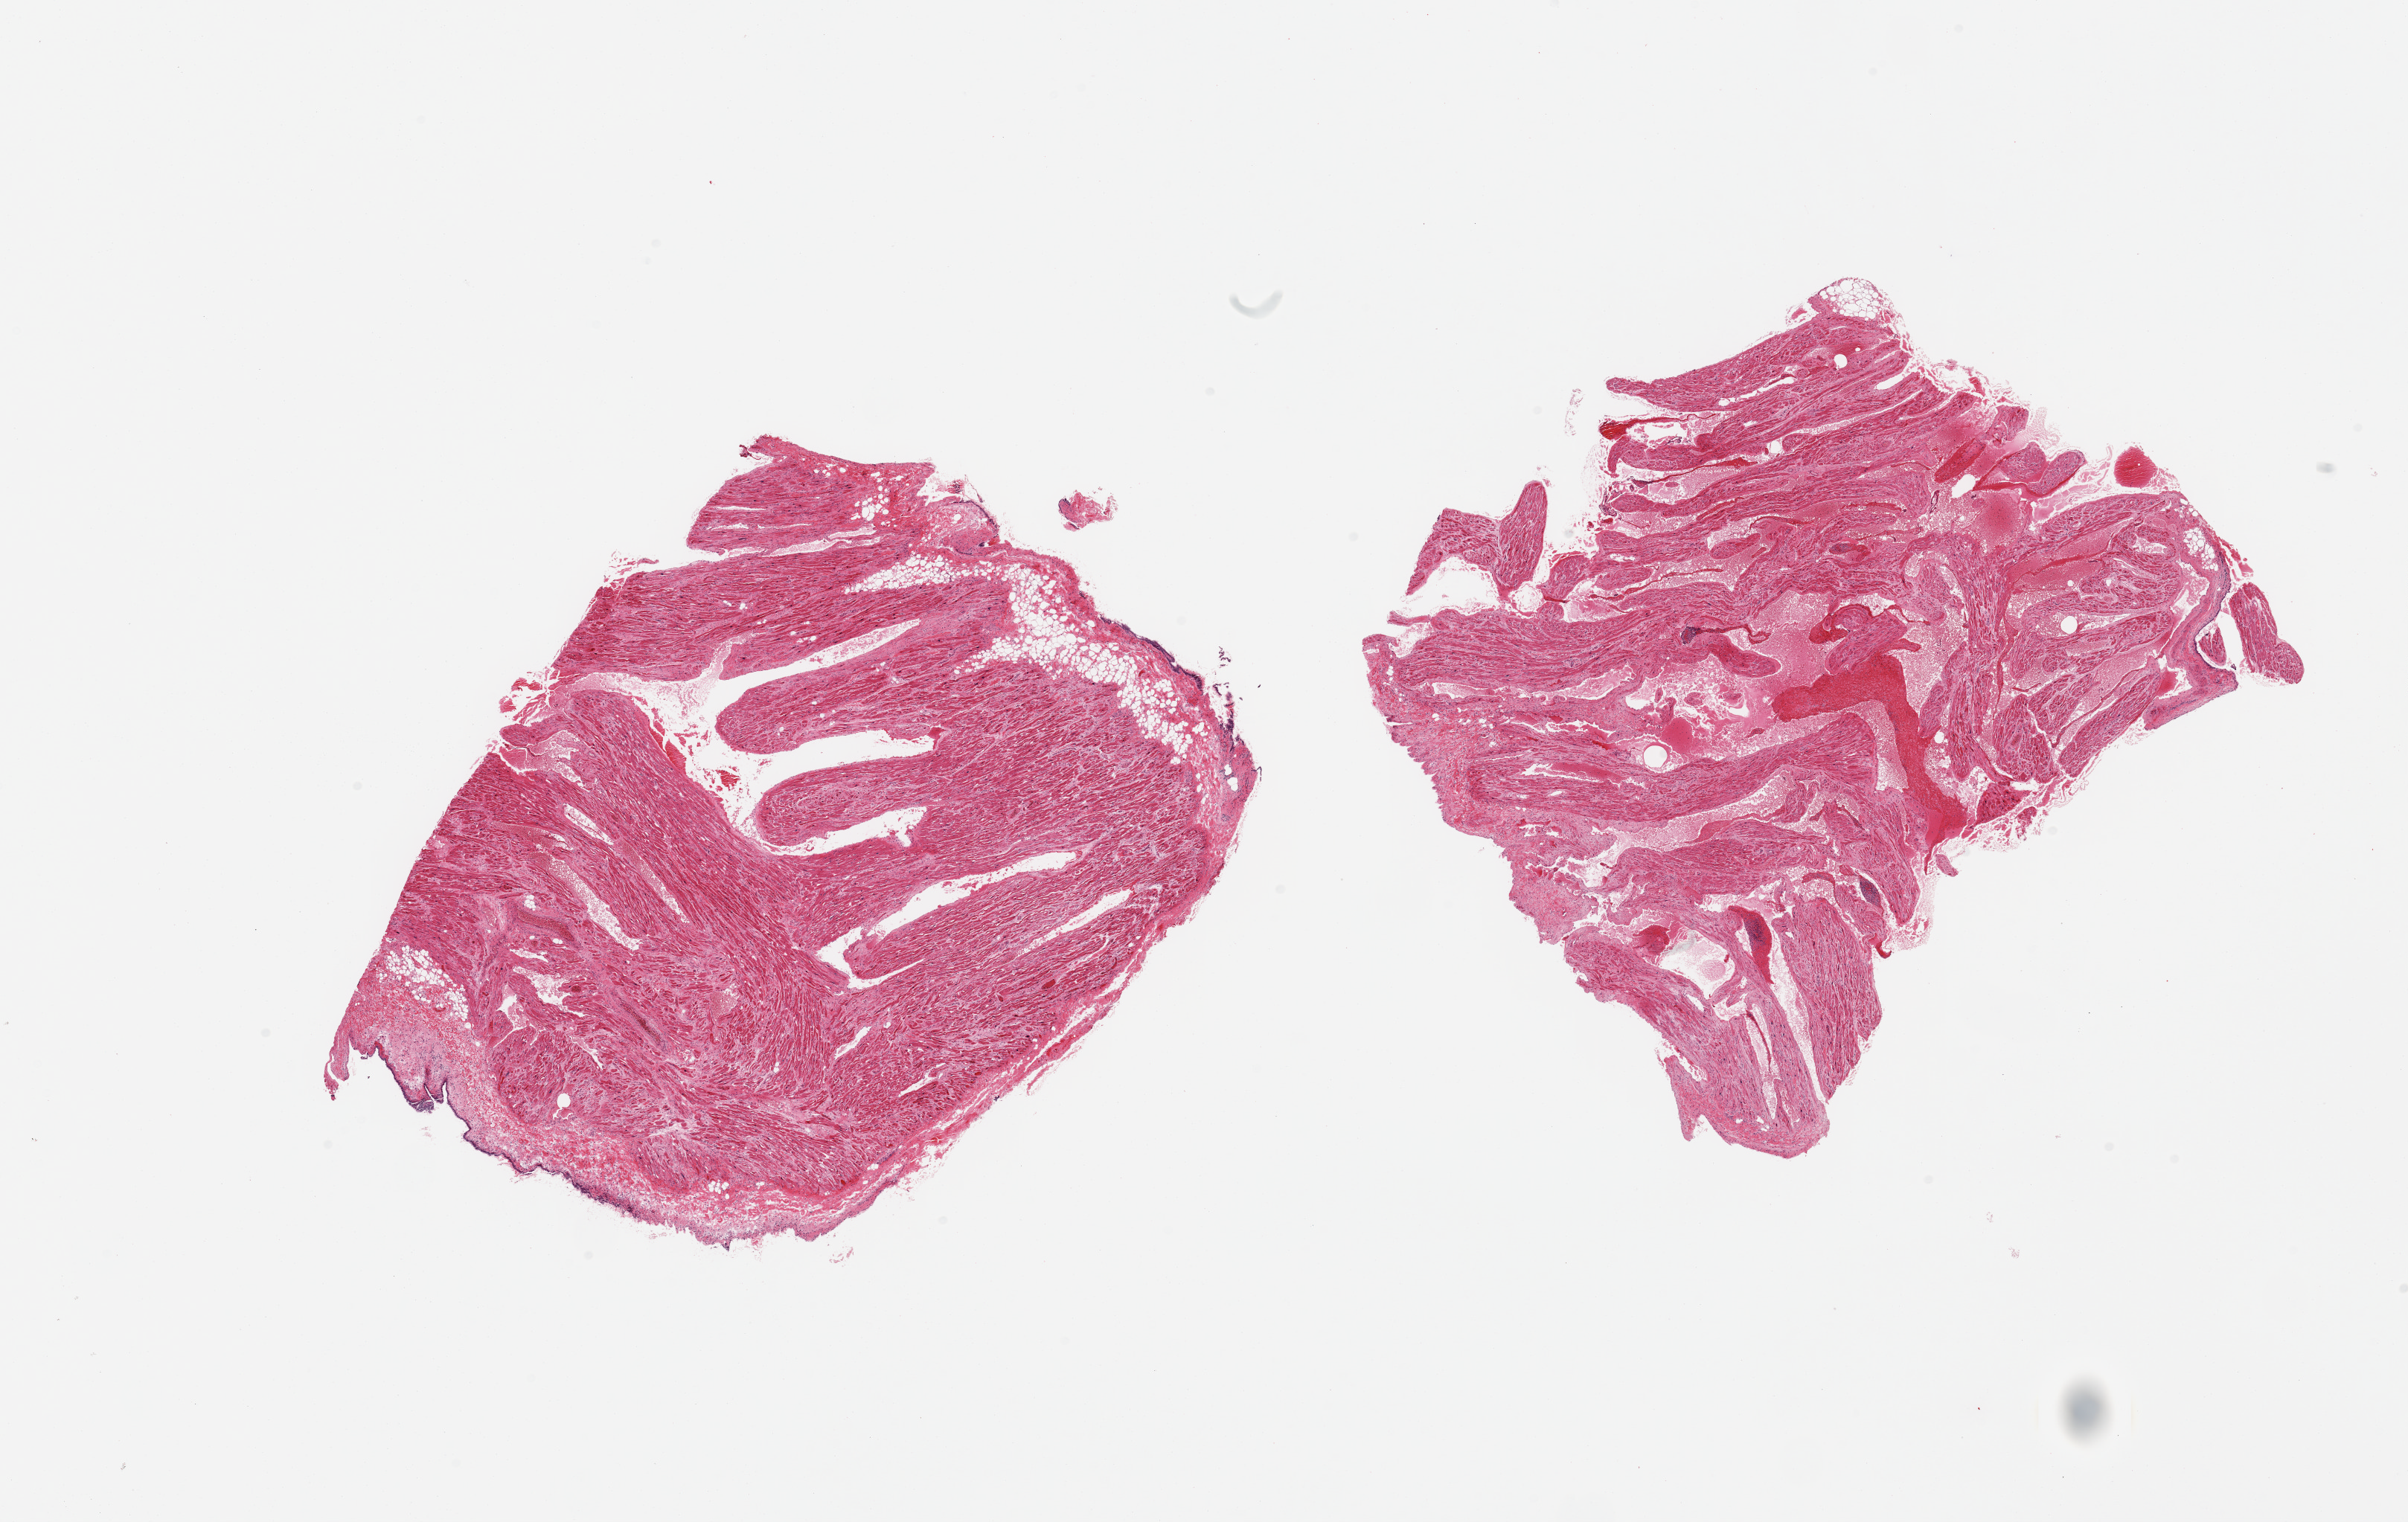
Haematoxylin and eosin whole-slide image, brightfield, a low-resolution overview of the entire scanned area, about 25.6 x 16.2 mm; PAXgene-fixed, paraffin-embedded tissue; sampled site (target tissue): auricular appendage; donor tissue sample. Donor: male.
* review note (as recorded): 2 pieces, no abnormalities